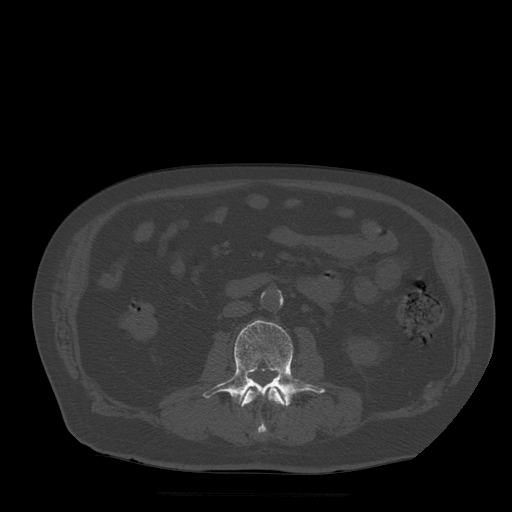
CT including the spine, one axial slice. Position 145 of 522 along the scan axis. Bone window (W 1800 / L 400 HU). 1.25 mm slice thickness. 512 × 512 image matrix, field of view 420 × 420 mm. Patient age 72 years. From the clinical record (not read from this slice): primary cancer: prostate.
Outlined on this slice (semi-automatic segmentation, software-assisted and operator-edited):
- L2 vertebra: bounding box [x1, y1, x2, y2] px = [241, 383, 286, 433]
- L3 vertebra: [203, 321, 326, 407]